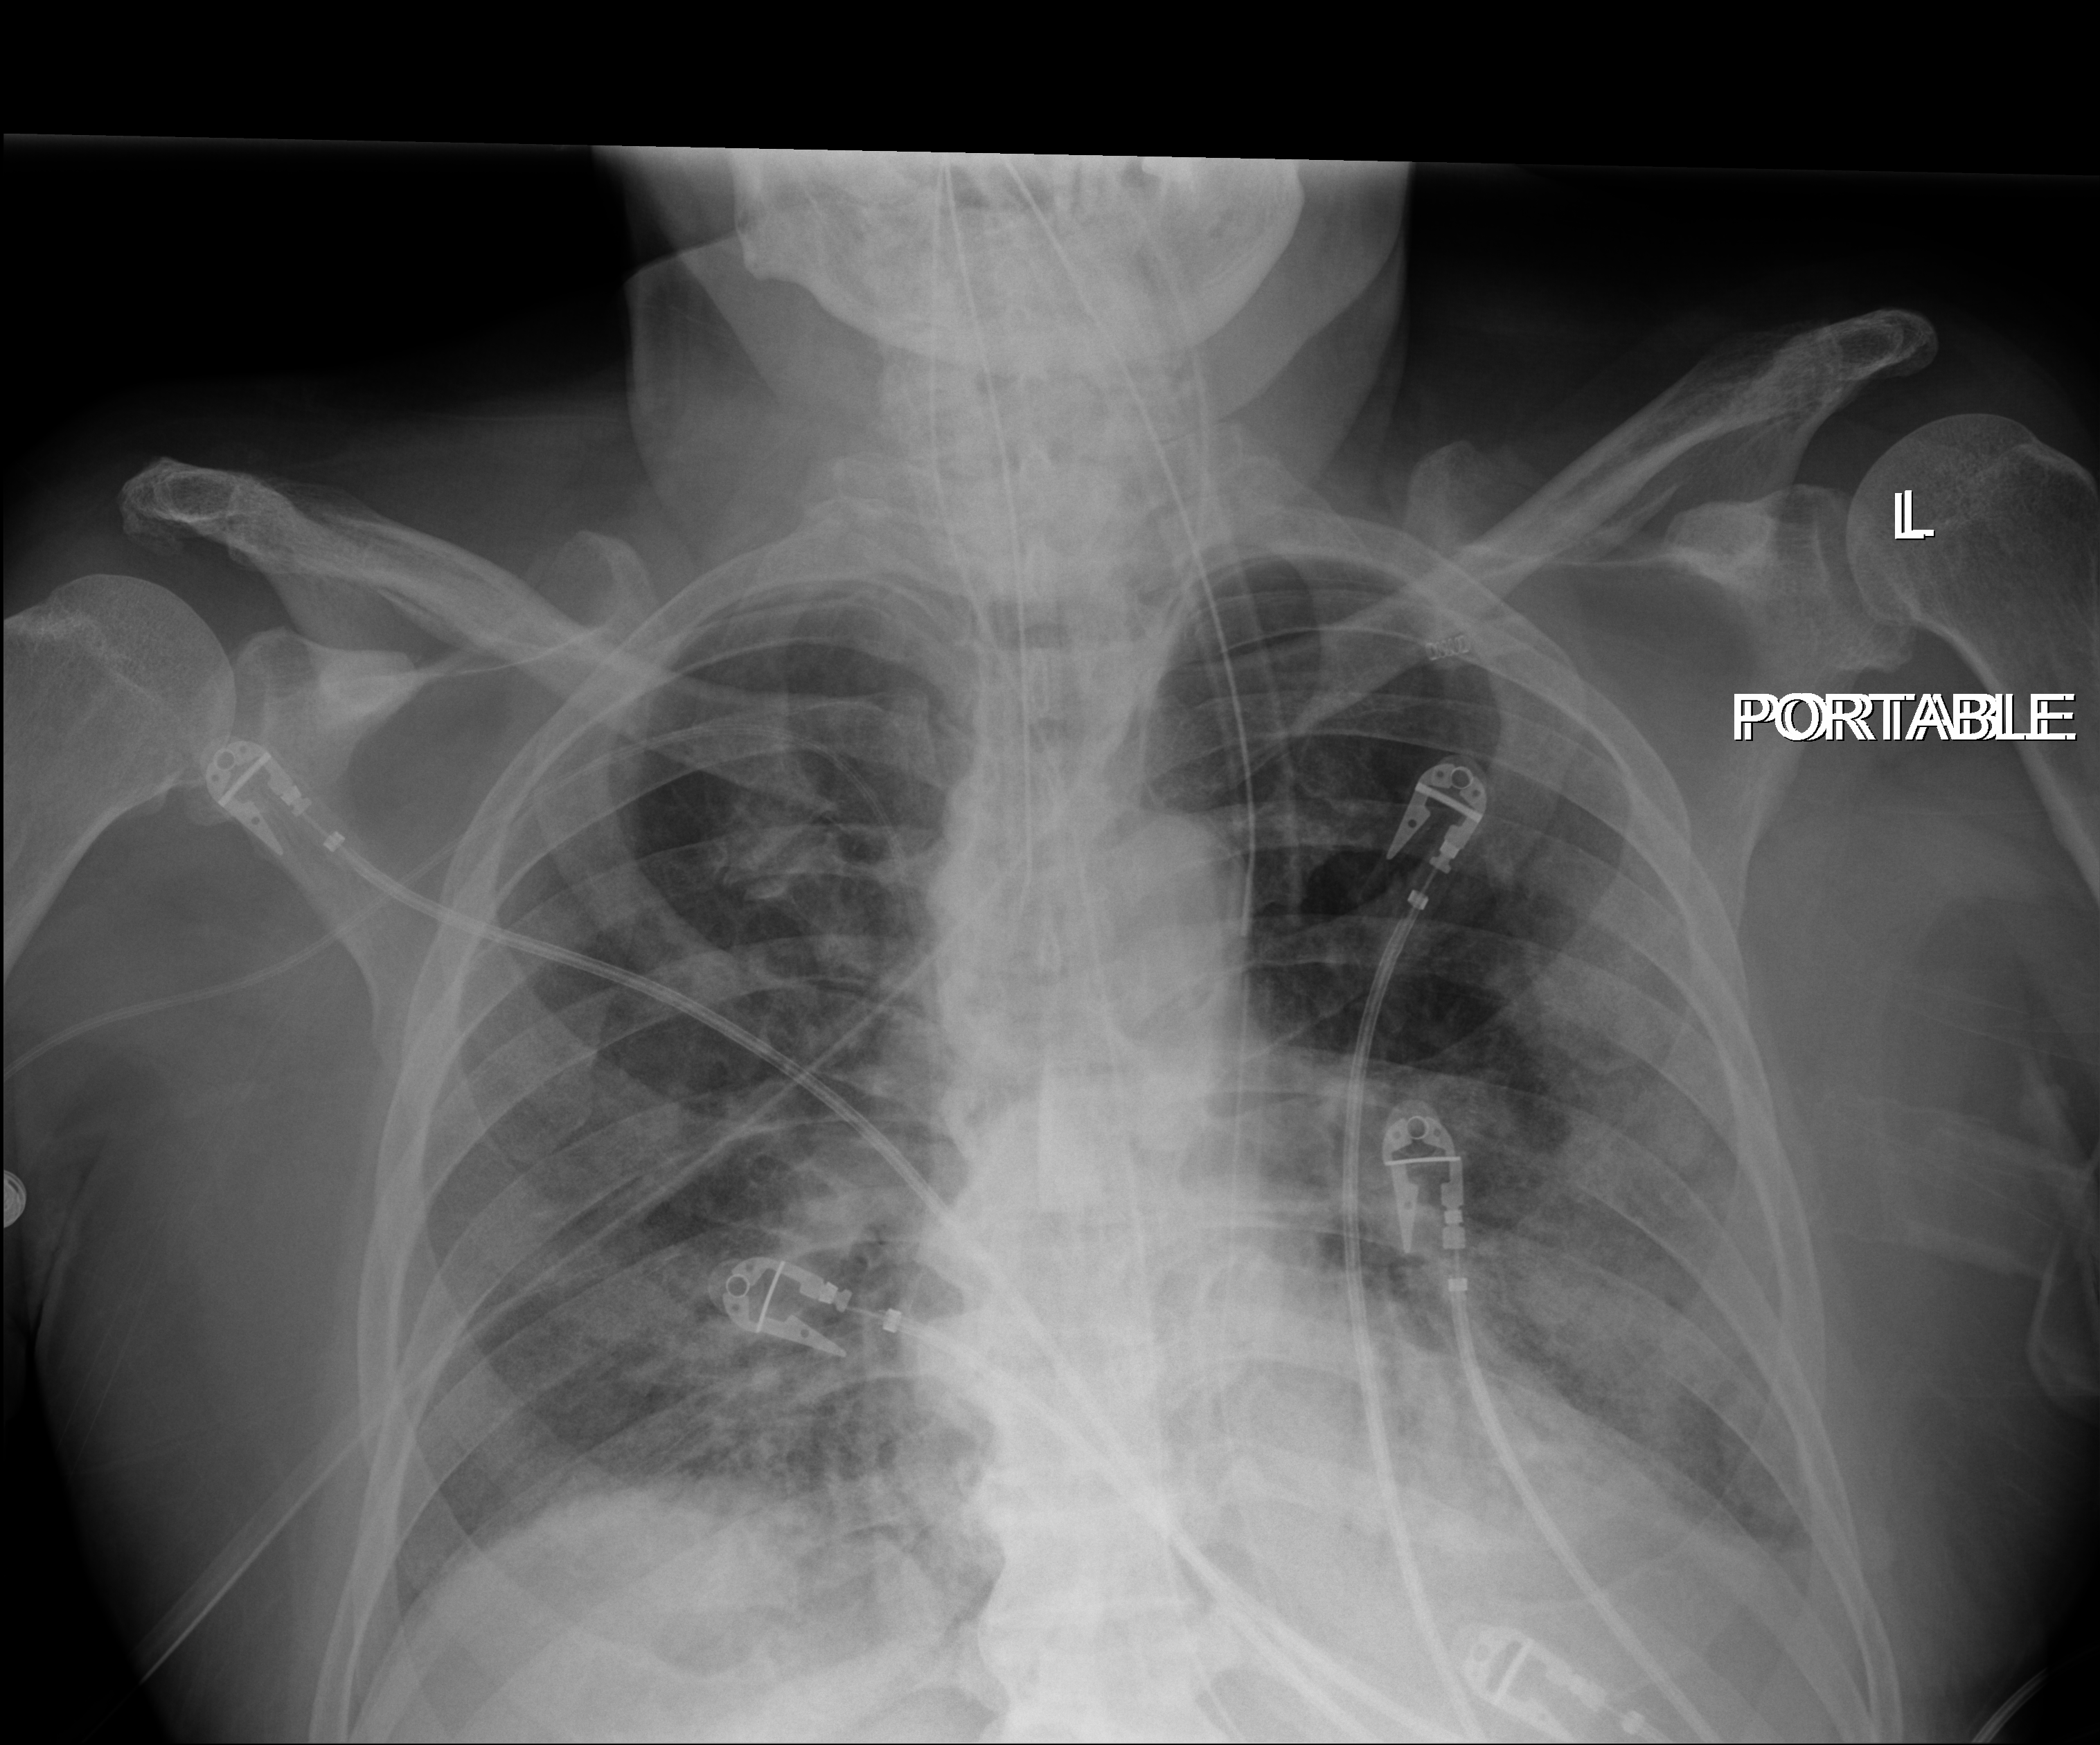
Portable chest radiograph; anteroposterior (AP) projection. Male patient hospitalised with COVID-19, age 75–90 years.
Admission-level facts for this patient (not findings on this image; timing relative to this image not recorded): other chronic lung disease (admission record): no; smoking status (admission record): former; admitted to intensive care during this hospital stay: yes.